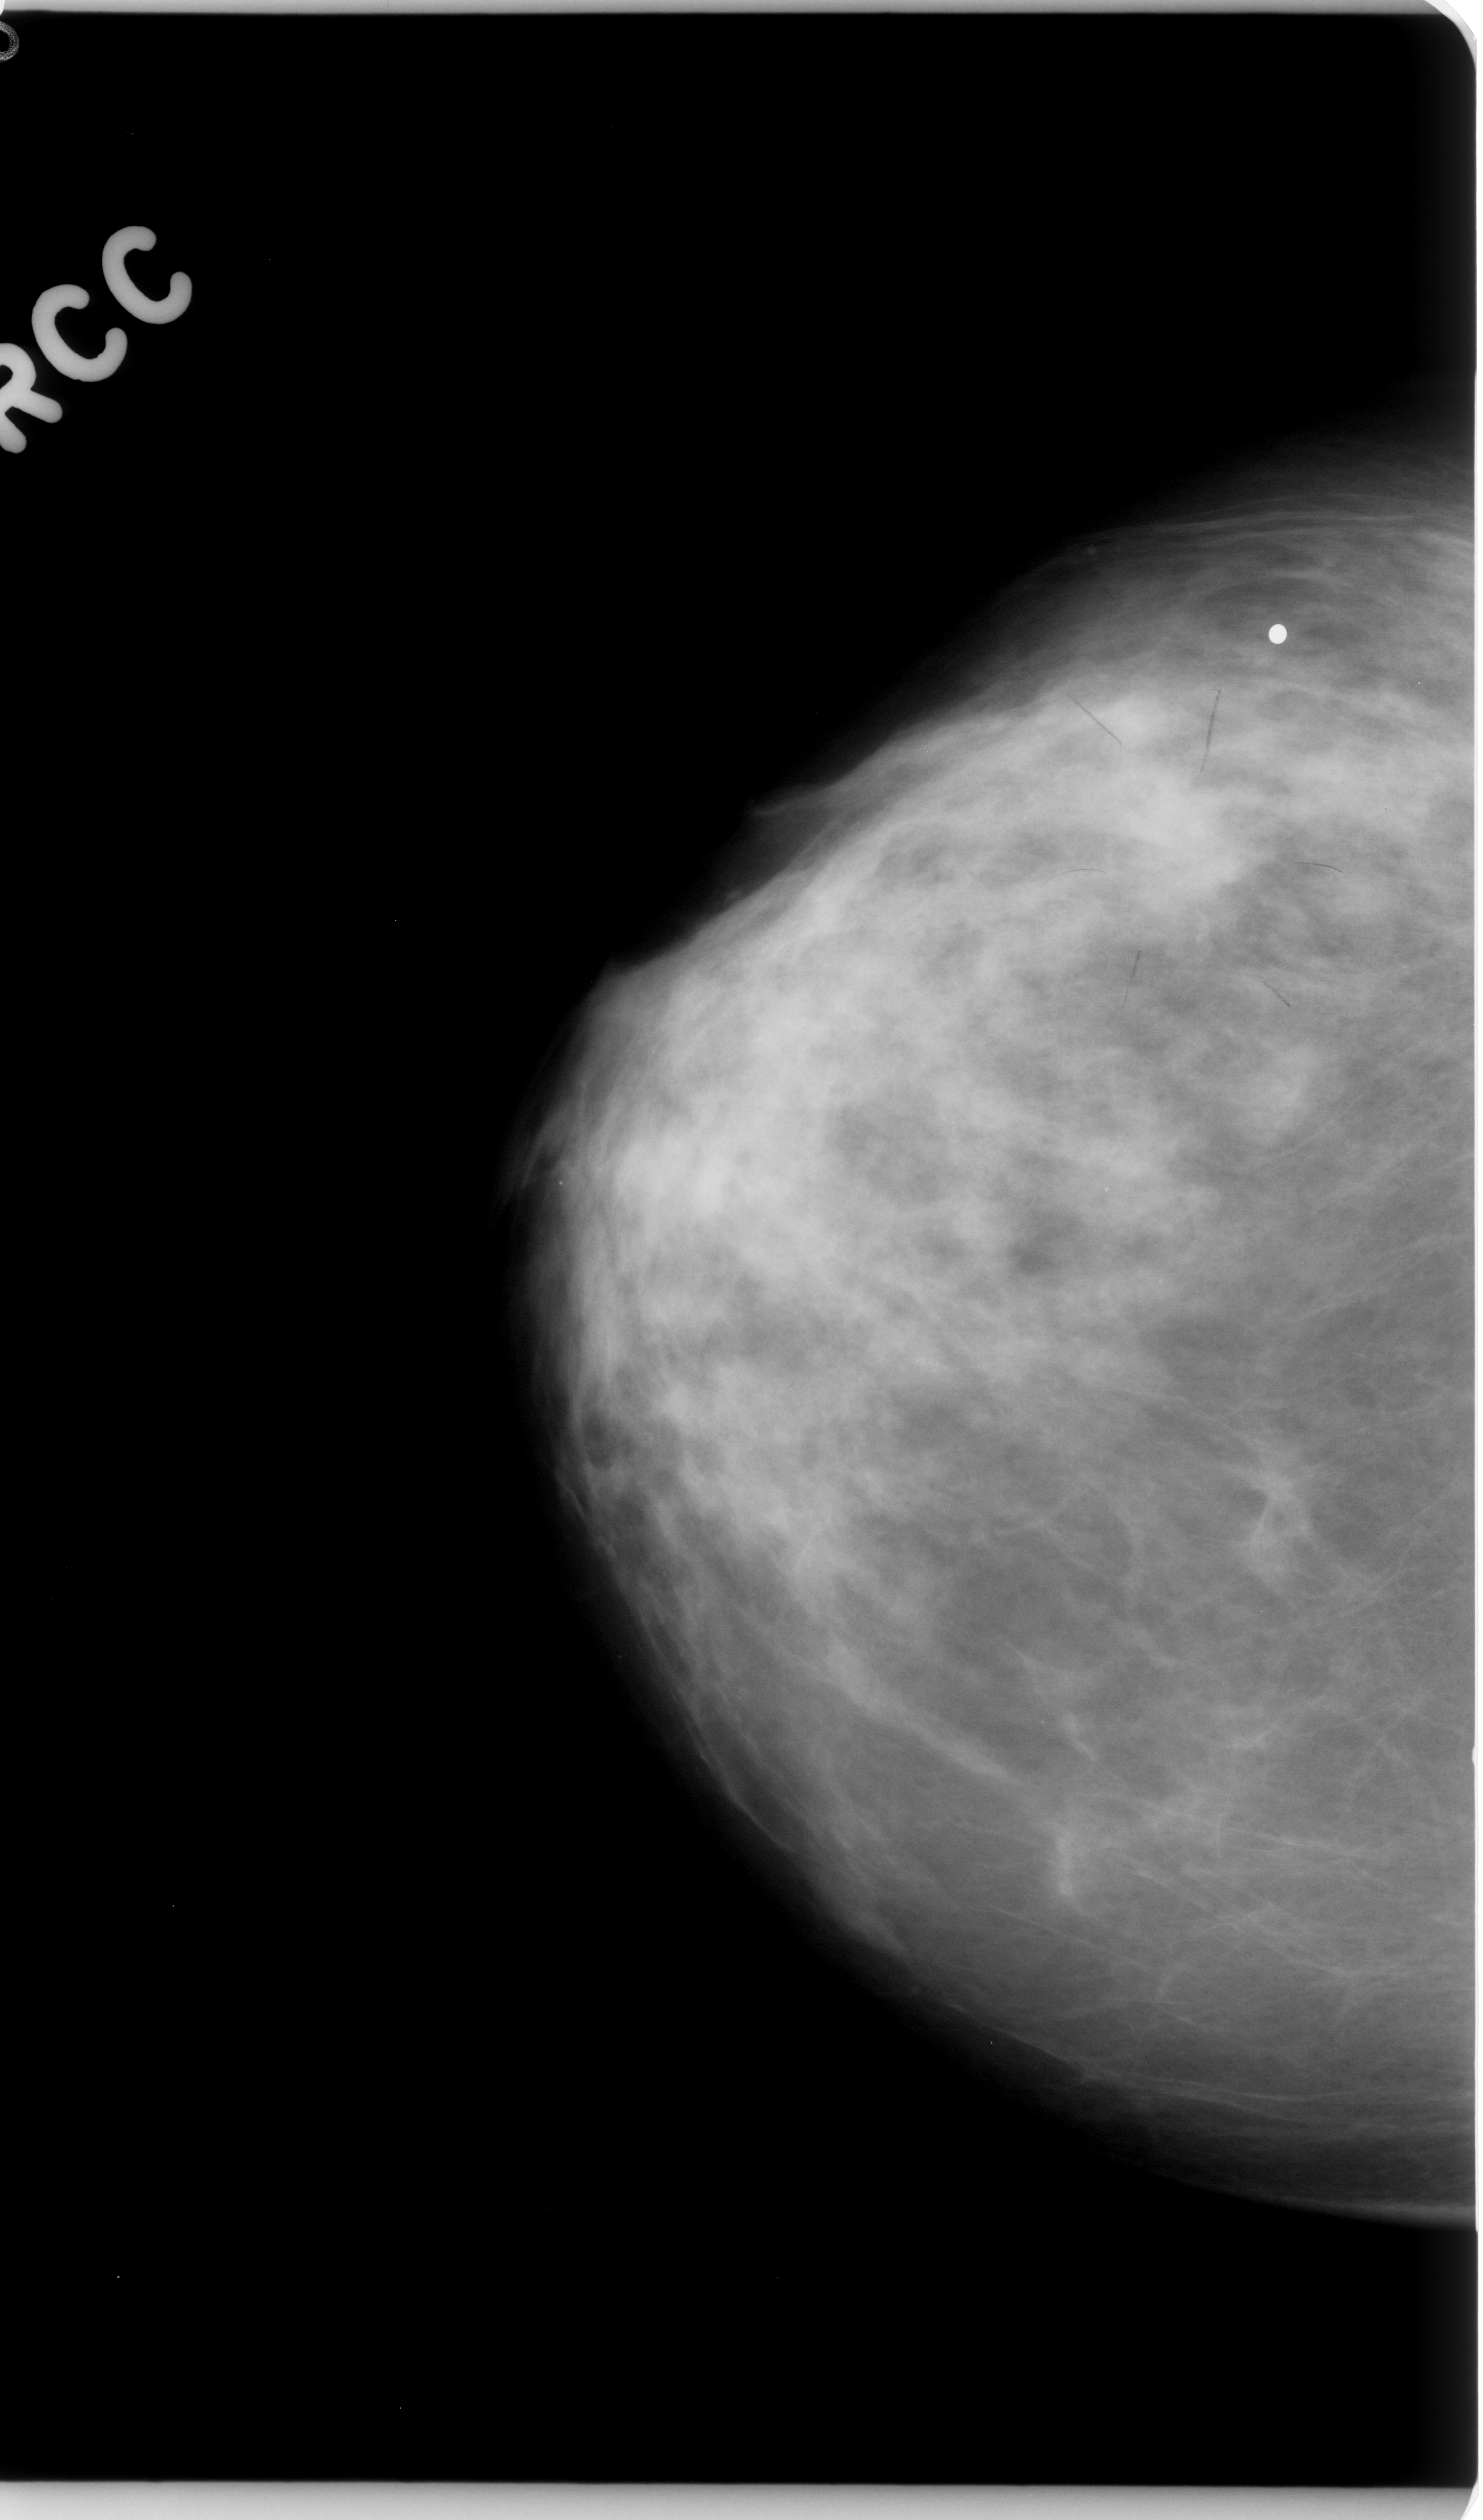
Mammogram (digitized film); right breast; CC view; breast composition: scattered fibroglandular densities (BI-RADS density category 2 of 4).
- Radiologist-marked abnormalities on this image: mass, shape irregular, margins ill defined; BI-RADS assessment category 4; pathology (as recorded): malignant.